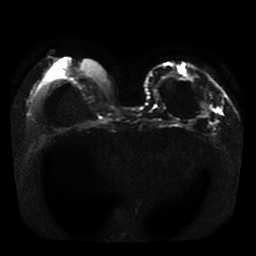
Breast MRI, one axial slice; position 11 of 41 along the scan axis; diffusion-weighted series; image 2 of 4 stored at this slice position (different b-values; order by instance number); 1.5 T; 5 mm slice thickness; 256 × 256 image matrix, field of view 330 × 330 mm. Female patient.
Structures marked on this image (expert manual segmentation):
- tumour on diffusion-weighted imaging: box from (x=202, y=104) to (x=210, y=117) px